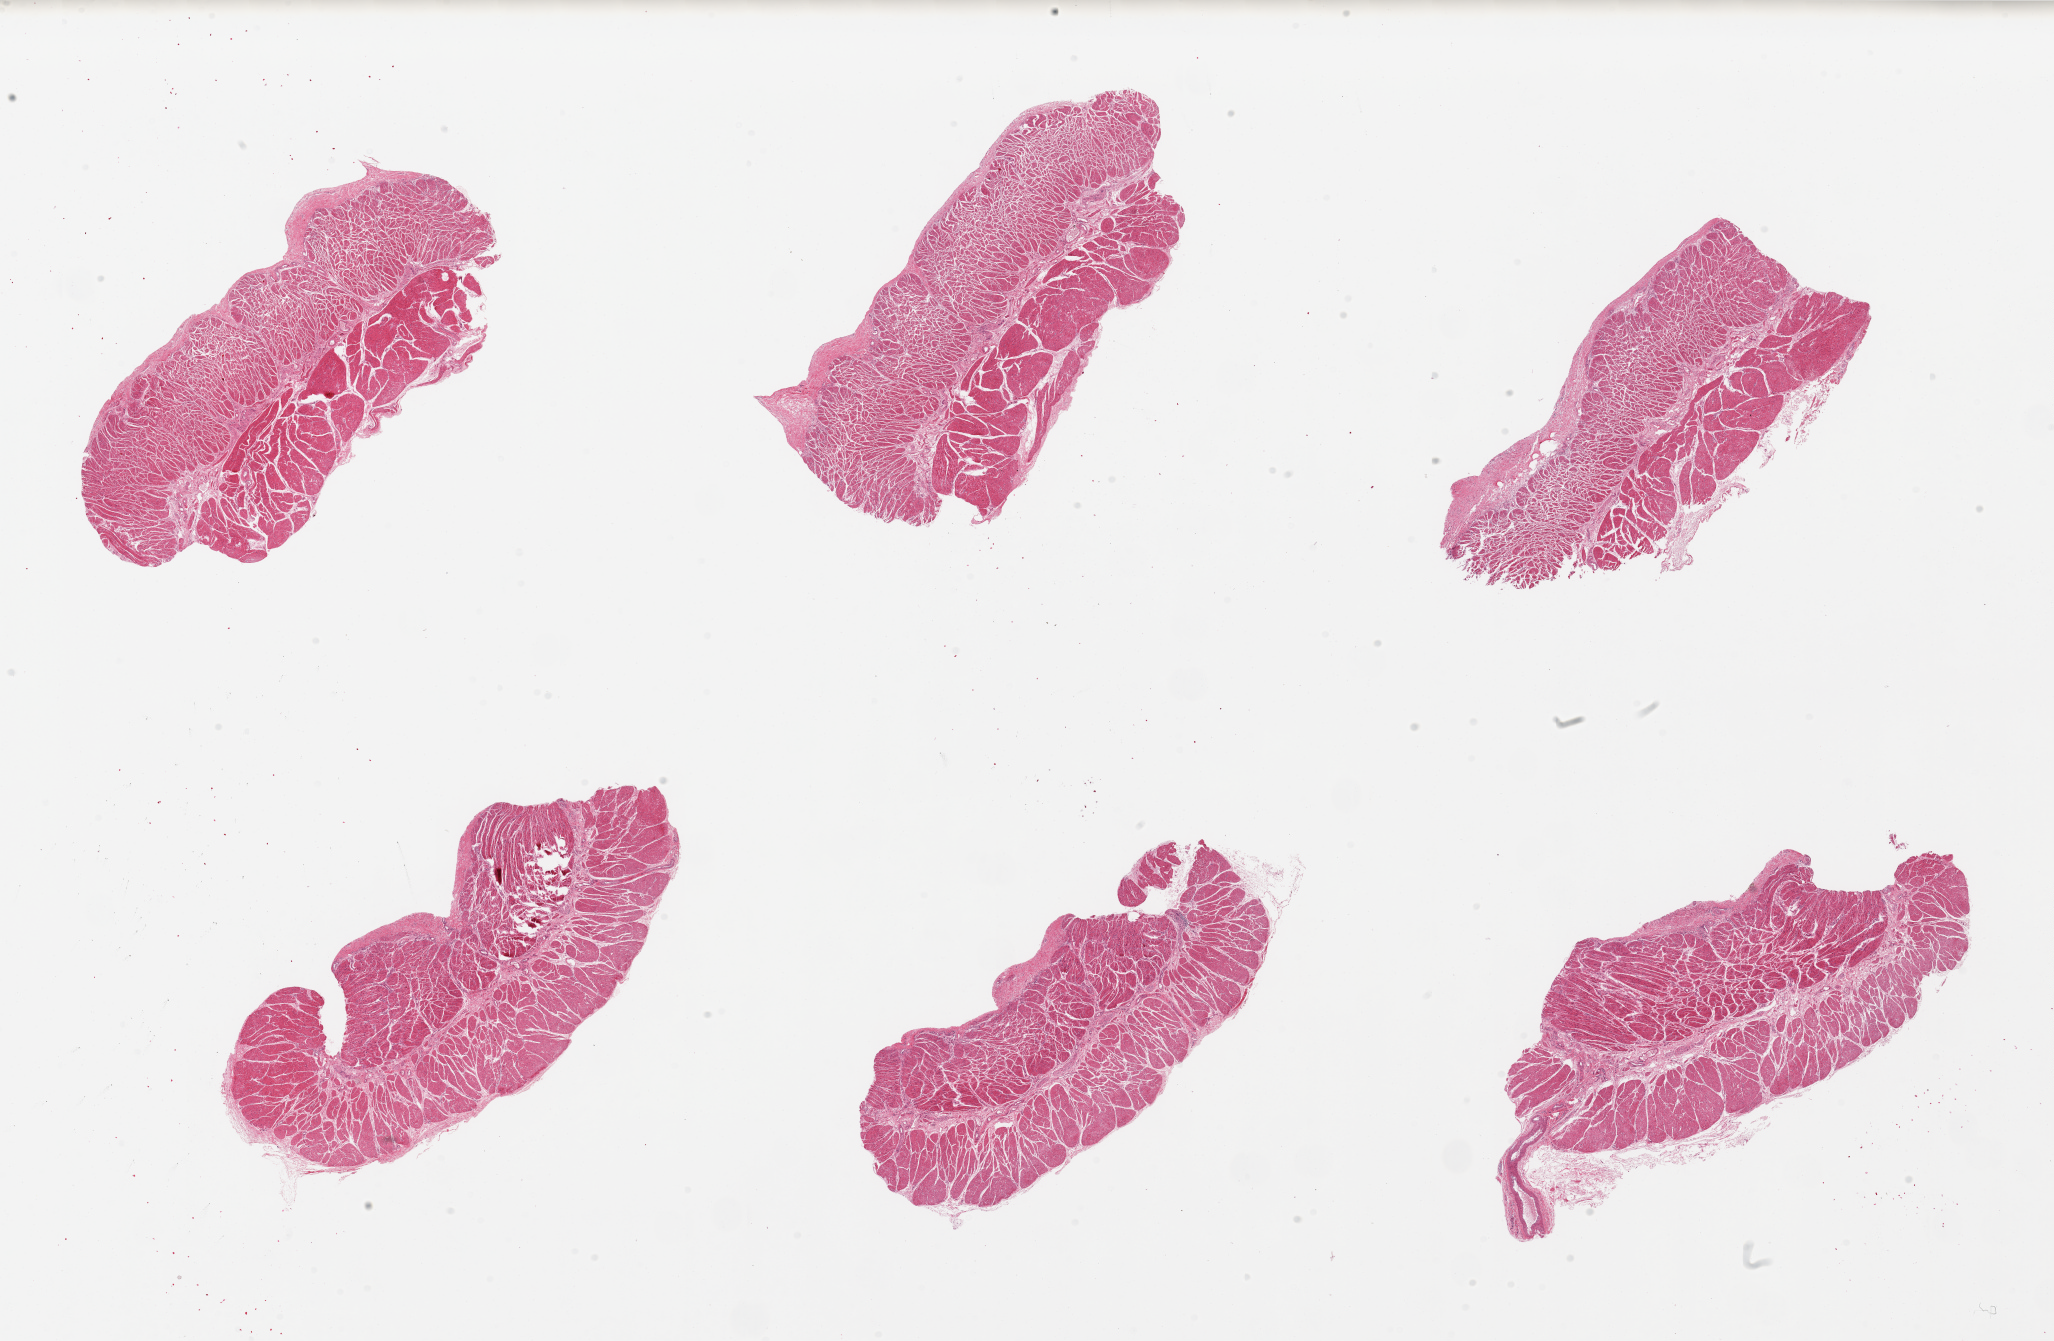
Haematoxylin and eosin whole-slide image — shown as a low-resolution overview of the whole scanned area (about 32.5 x 21.2 mm). PAXgene-fixed paraffin-embedded (PFPE) section. Sampled site (target tissue): esophageal muscle. Tissue donor sample. Donor sex: male.
• reviewer comment on this tissue sample: 6 pieces, well trimmed